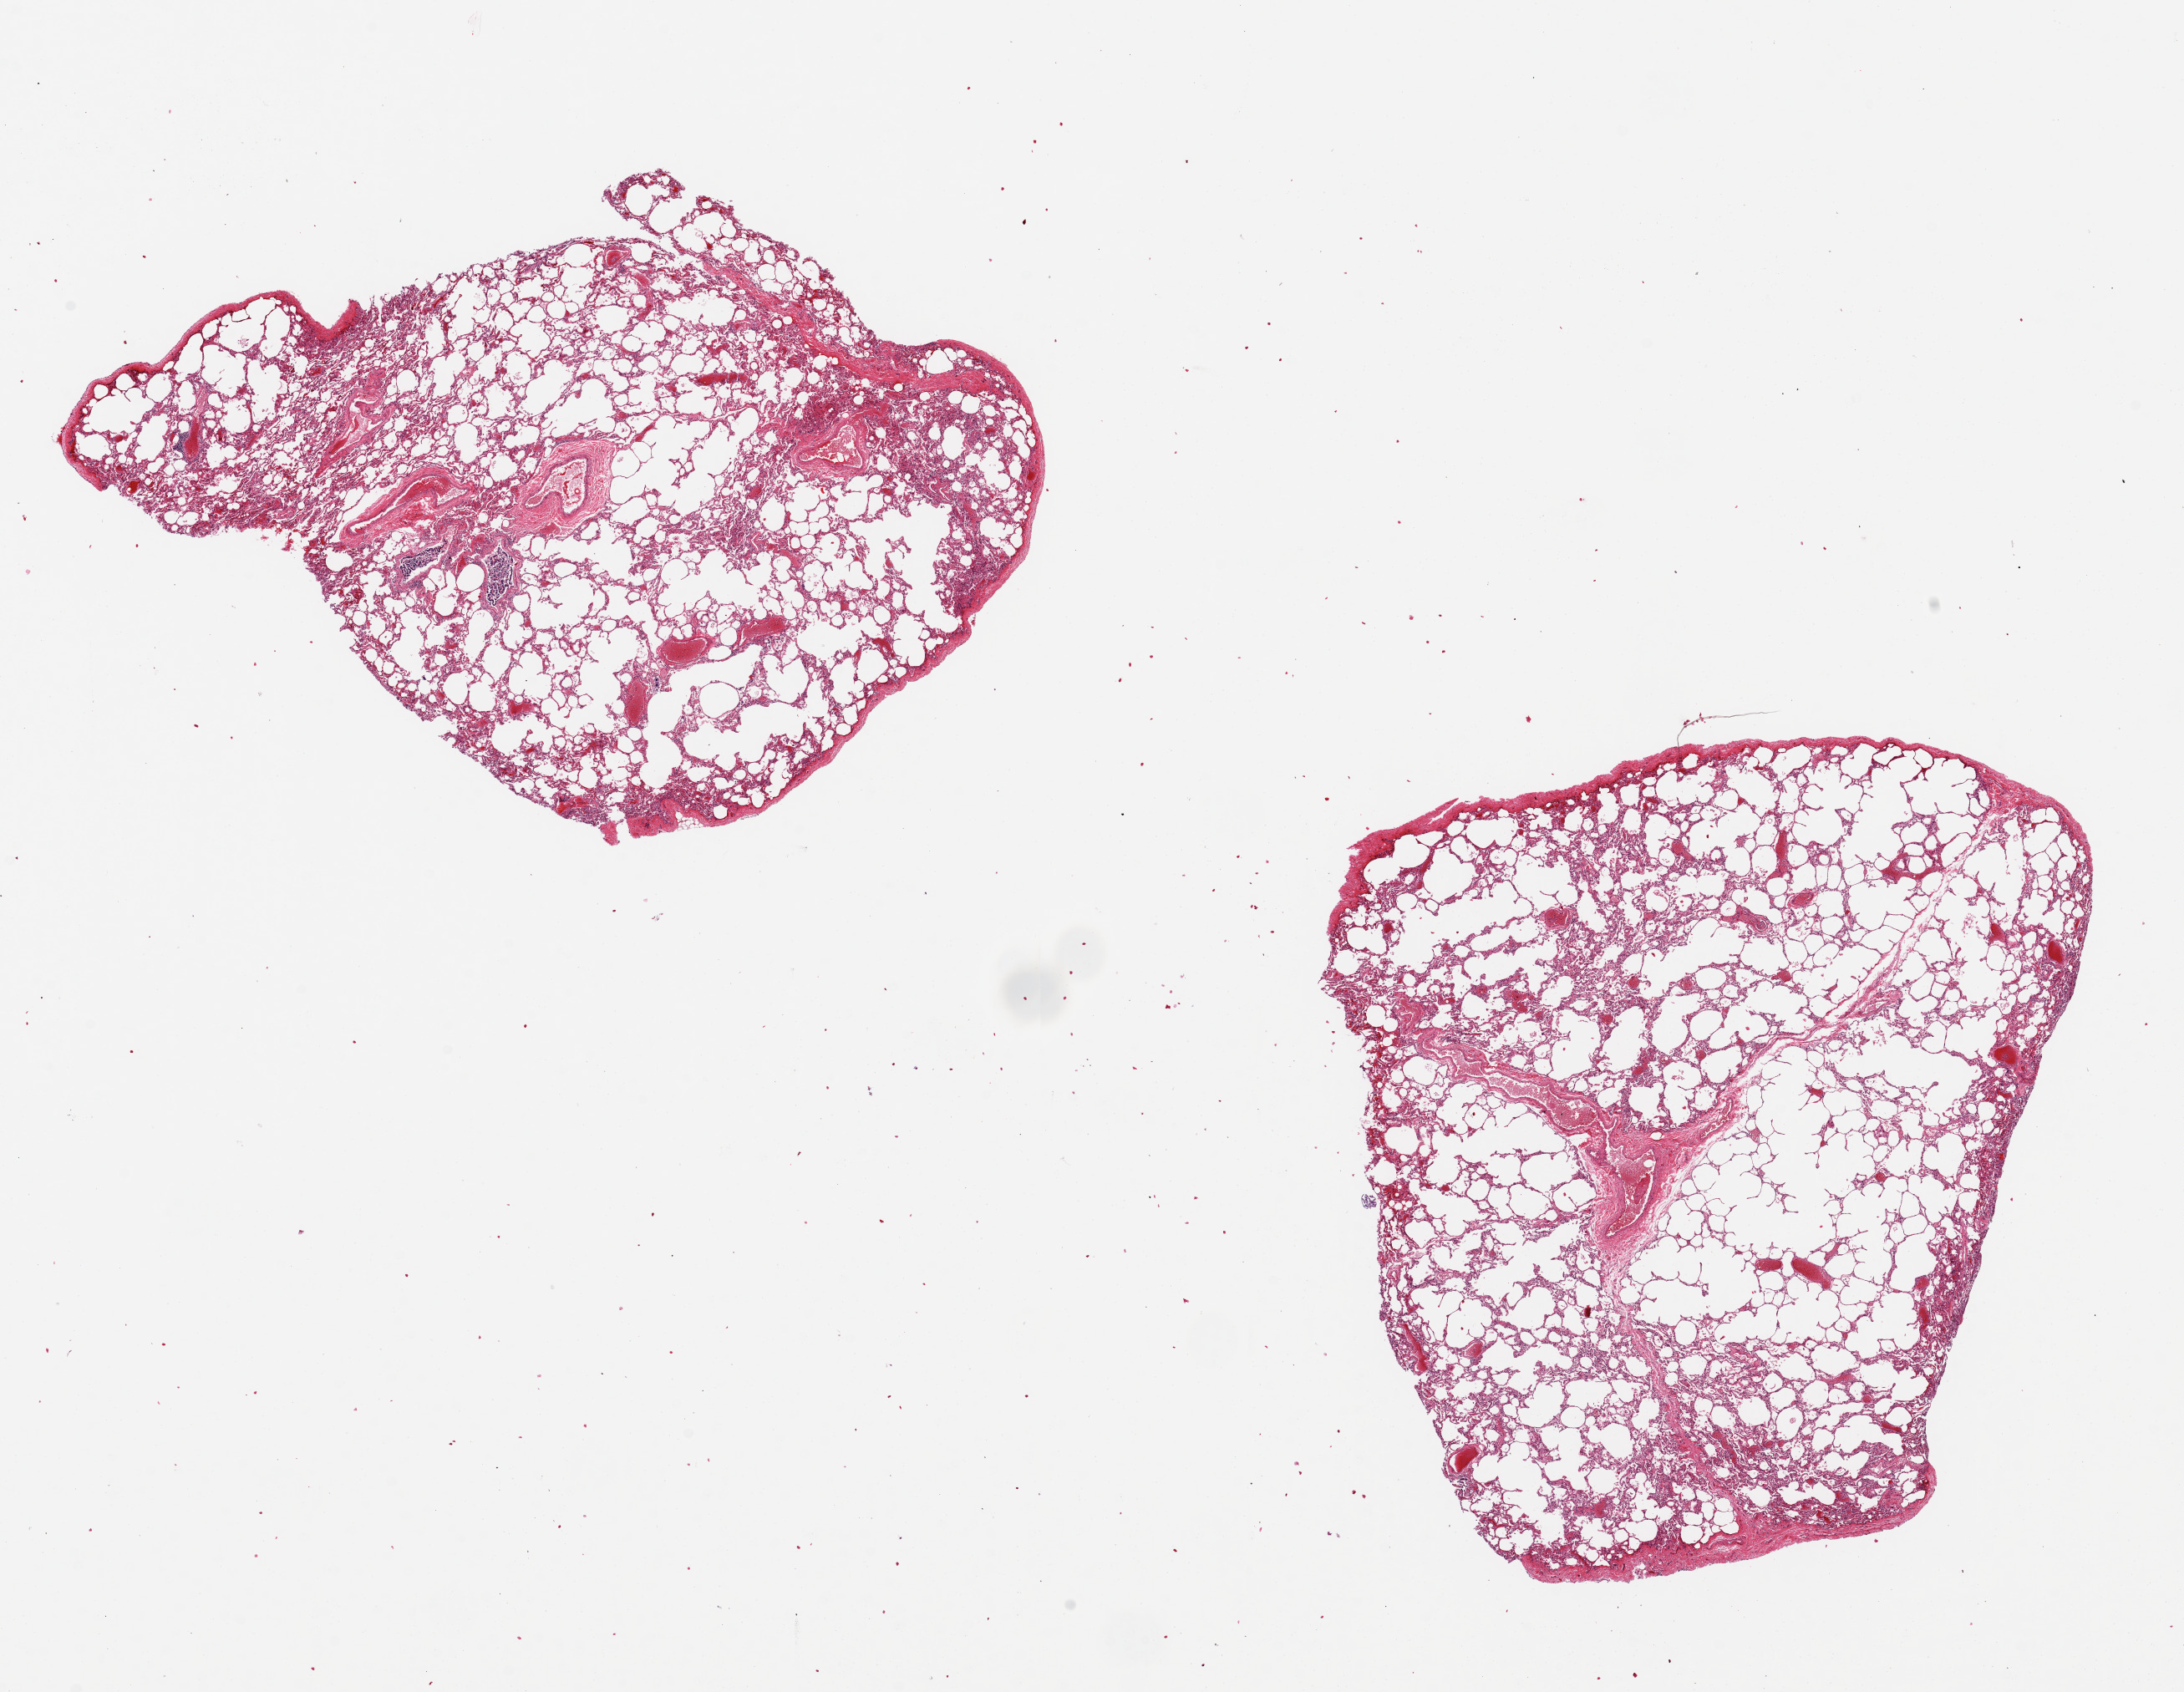
Whole-slide image, hematoxylin and eosin (H&E) stain, brightfield — whole scanned area (about 20.7 x 16.0 mm) shown as a low-resolution overview. PAXgene-fixed, paraffin-embedded tissue. Section of lung (target tissue). Tissue donor sample. Donor sex: male.
Pathologist's review note for this sample: 2 pieces 7x7 & 6x6 mm; good alveolar structure; bronchial epithelium autolyzed.